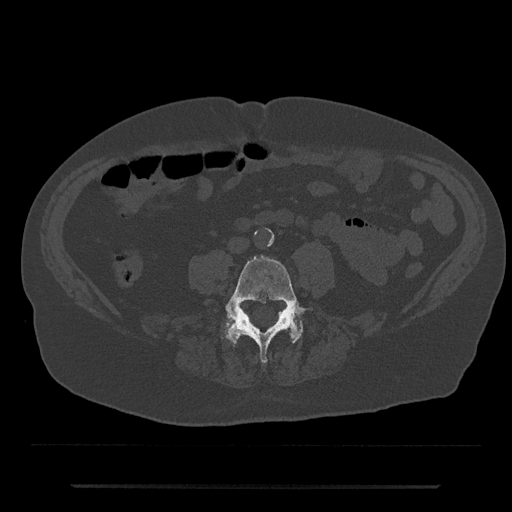
CT including the spine, one axial slice. Slice 345 of 797 in the series (ordered by position). Reconstruction kernel Br40s/3. 120 kVp. Bone window (W 1800 / L 400 HU). 512 × 512 image matrix, field of view 434 × 434 mm. Patient: male, 80 years. Case-level facts recorded for this patient, not image findings: primary cancer: prostate; vertebrae with lytic lesions (as recorded): L1, T11.
Outlined on this slice (semi-automatically segmented with operator editing):
- L4 vertebra: bounding box <225,255,314,363> (left, top, right, bottom; pixels)
- L5 vertebra: <225,317,303,343>